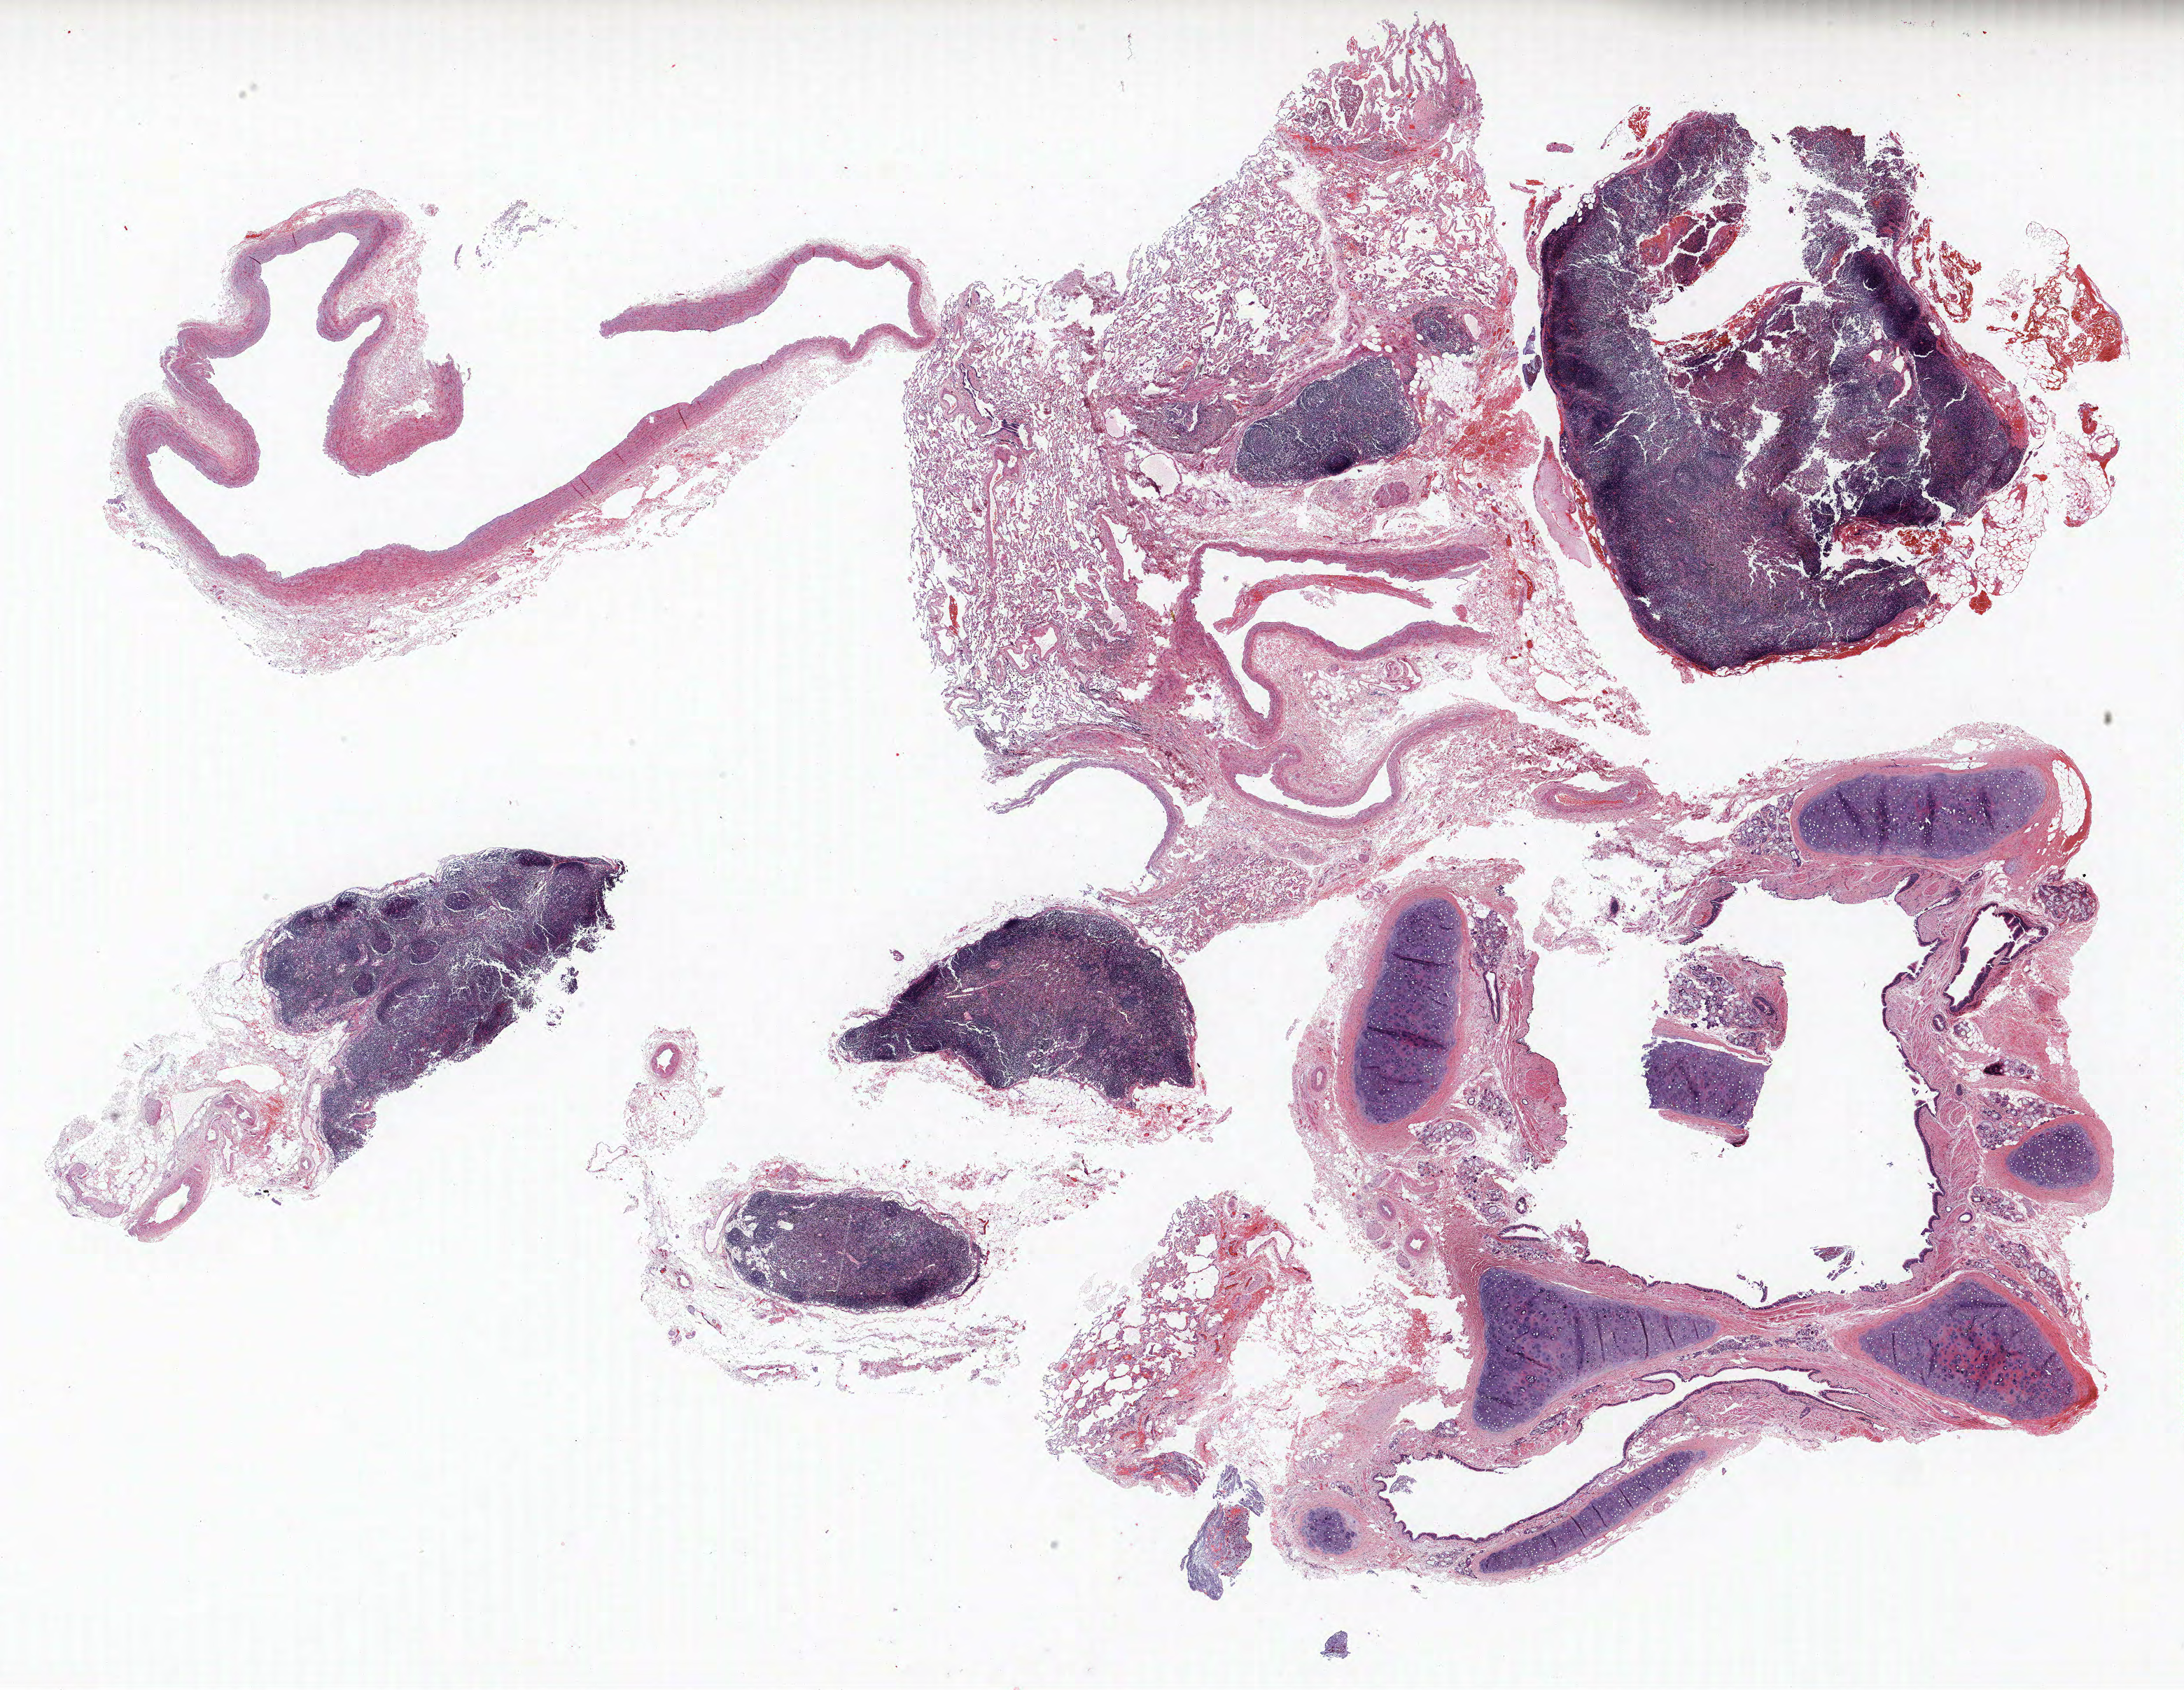
H&E whole-slide image — shown as a low-resolution overview of the whole scanned area (about 25.0 x 19.3 mm, from a 40x scan), formalin-fixed paraffin-embedded (FFPE) section, lung. Female patient, aged 58 at enrolment. Grade: well differentiated (G1).
ICD-O-3 topography: lower lobe of lung (C34.3). Stage (AJCC 6th edition): IB. Participant's lung-cancer diagnosis: Adenocarcinoma, NOS. Primary tumour location (clinical record): right lower lobe. Tumour size (pathology): 10 mm.